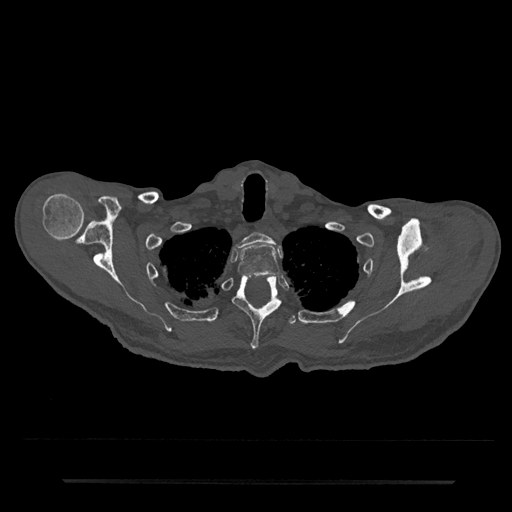
CT including the spine, one axial slice; slice 667 of 797 in the series (ordered by position); 120 kVp; bone window (W 1800 / L 400 HU); 0.5 mm slice thickness; 512 × 512 image matrix, field of view 427 × 427 mm. Male patient, age 74 years. Case-level facts recorded for this patient, not image findings: primary cancer: prostate.
Structures marked on this image (semi-automatically segmented with operator editing):
- T1 vertebra: bounding box (x1, y1, x2, y2) in pixels: (237, 232, 275, 249)
- T2 vertebra: (237, 244, 280, 276)
- T3 vertebra: (233, 275, 282, 350)
- T4 vertebra: (286, 315, 297, 326)